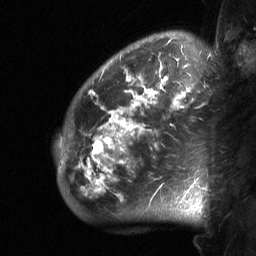
Breast MRI (dynamic contrast-enhanced), one sagittal slice. Position 51 of 64 along the scan axis. Dynamic contrast-enhanced study with each time point stored as its own series, time point 2 of 3 at this slice position (early post-contrast, ordered by acquisition time). 1.5 T. TE 4.8 ms, TR 27 ms. 2 mm slice thickness. 256 × 256 image matrix, field of view 200 × 200 mm. Patient: female, 50 years. Case-level facts recorded for this patient, not image findings: setting: breast cancer imaged before/during neoadjuvant chemotherapy; receptor status: HER2-positive.
Outlined on this slice (semi-automatically segmented with operator editing):
- analysis volume of interest (the breast-tissue region the enhancement analysis was run in; not a lesion): box from (x=56, y=62) to (x=218, y=222) px
- tumour enhancement mask (voxels above the 90 % enhancement threshold inside the analysis volume of interest): (x=79, y=64)–(x=208, y=195)